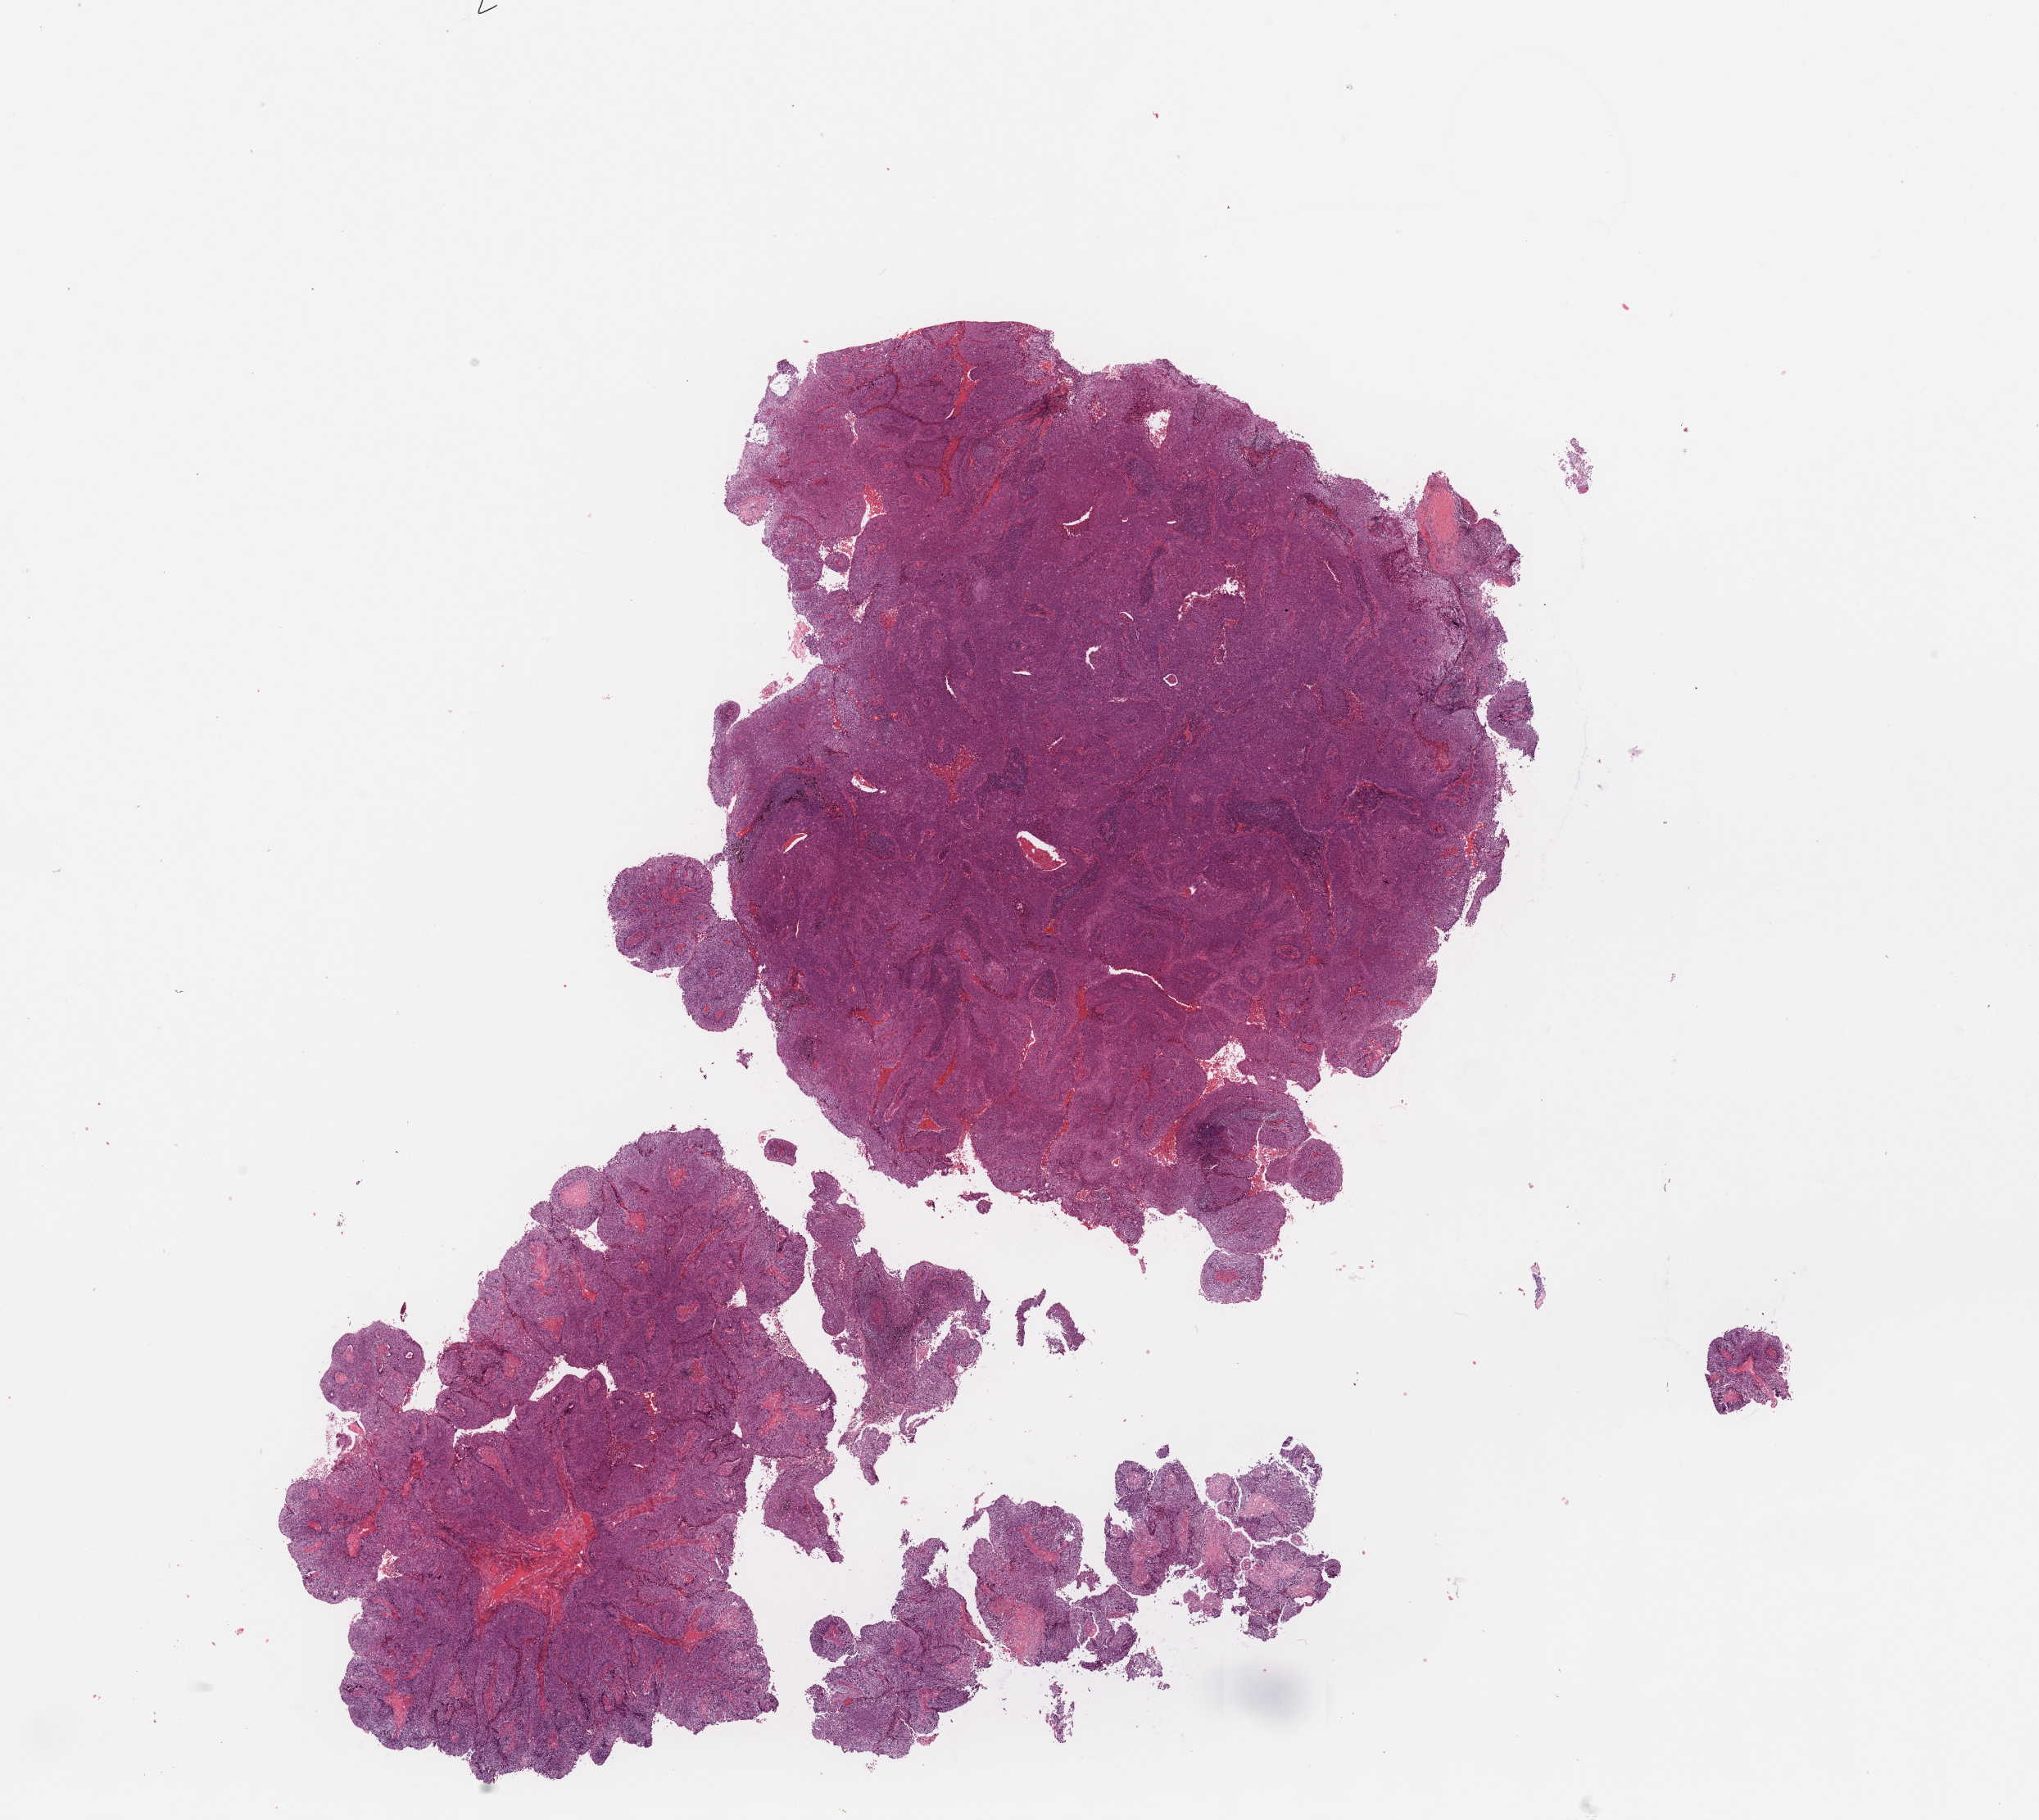
Digitized H&E-stained tissue section (whole slide) — shown as a low-resolution overview of the whole scanned area (about 19.7 x 17.6 mm, acquisition: 20x scan). Tumour tissue sample, sampled site: lung. Male, 59 y/o. Histologic grade: G3 (poorly differentiated). Composition of this section per pathologist review: tumour nuclei 80%, necrosis 3%.
Histologic diagnosis: Squamous cell carcinoma, NOS. AJCC pathologic stage: IIB. Primary tumour site (as recorded): left upper lobe.